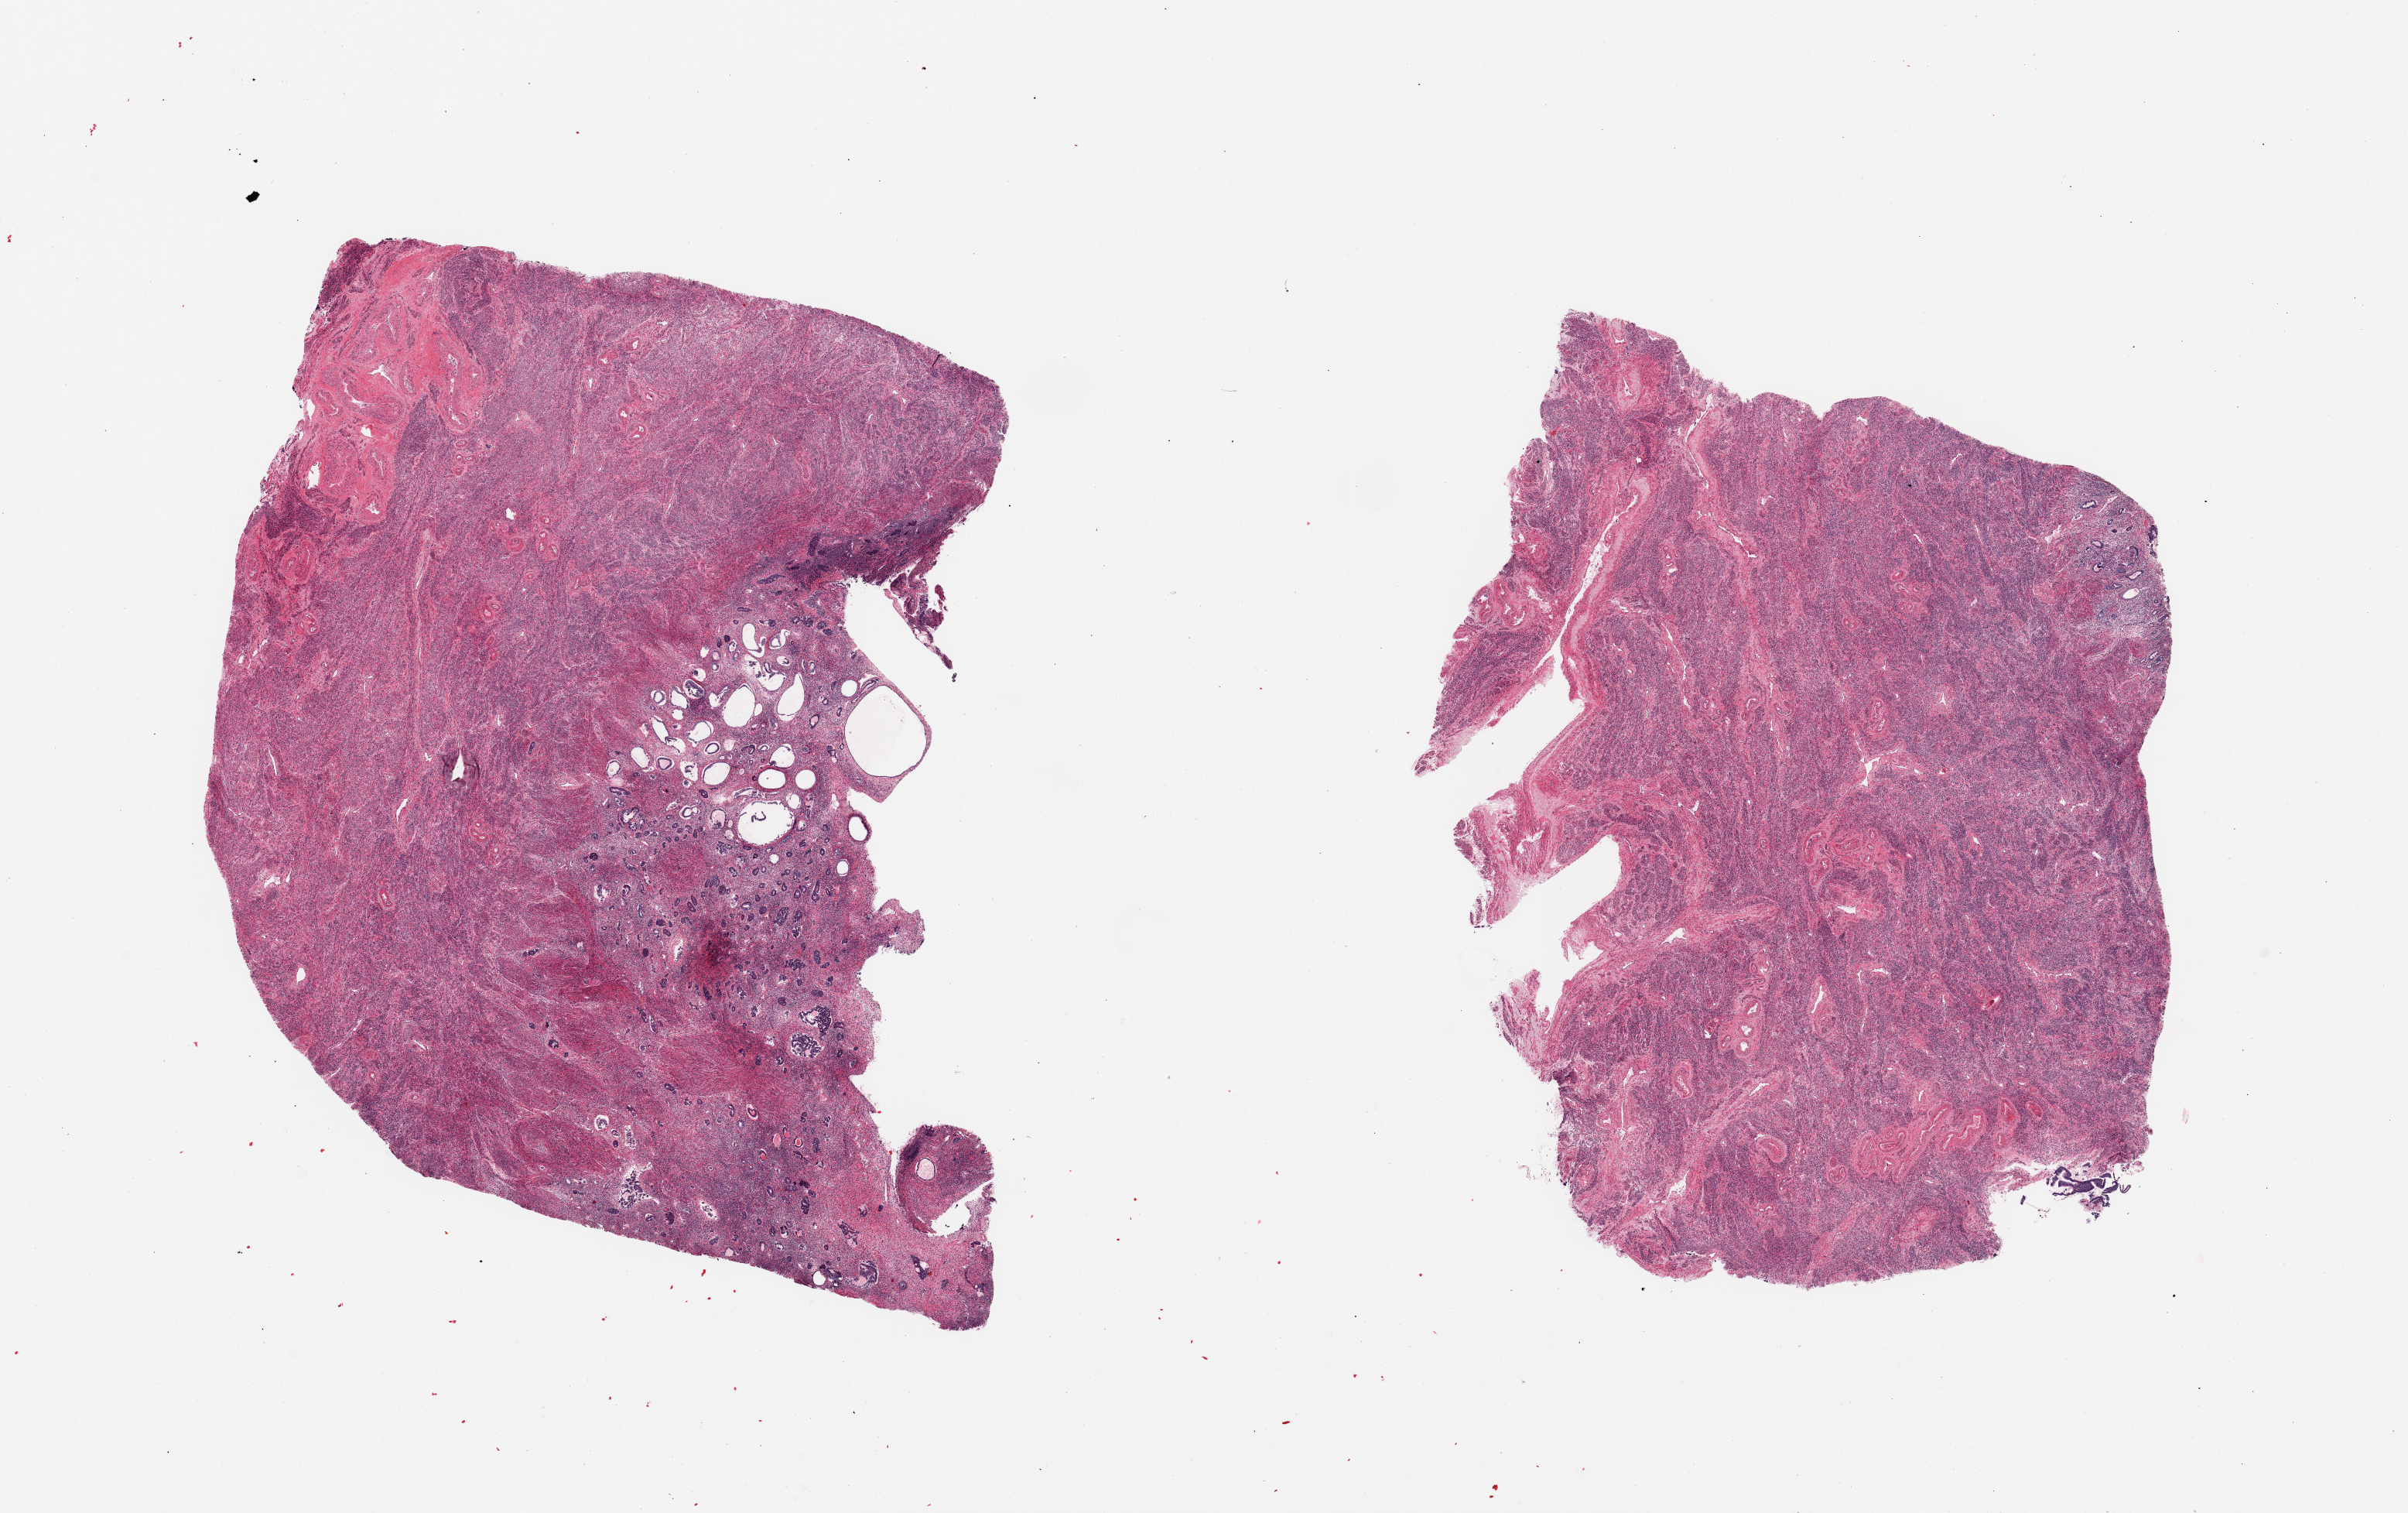
Whole-slide image, hematoxylin and eosin (H&E) stain, a low-resolution overview of the entire scanned area, about 24.6 x 15.5 mm (from a 20x scan), PAXgene-fixed paraffin-embedded (PFPE) section, target tissue: uterus, donor tissue sample.
Review note (as recorded): 2 pieces; 1 has 40% endometrium with cystic atrophy and adenomyosis; other is all myometrium (in this cut).